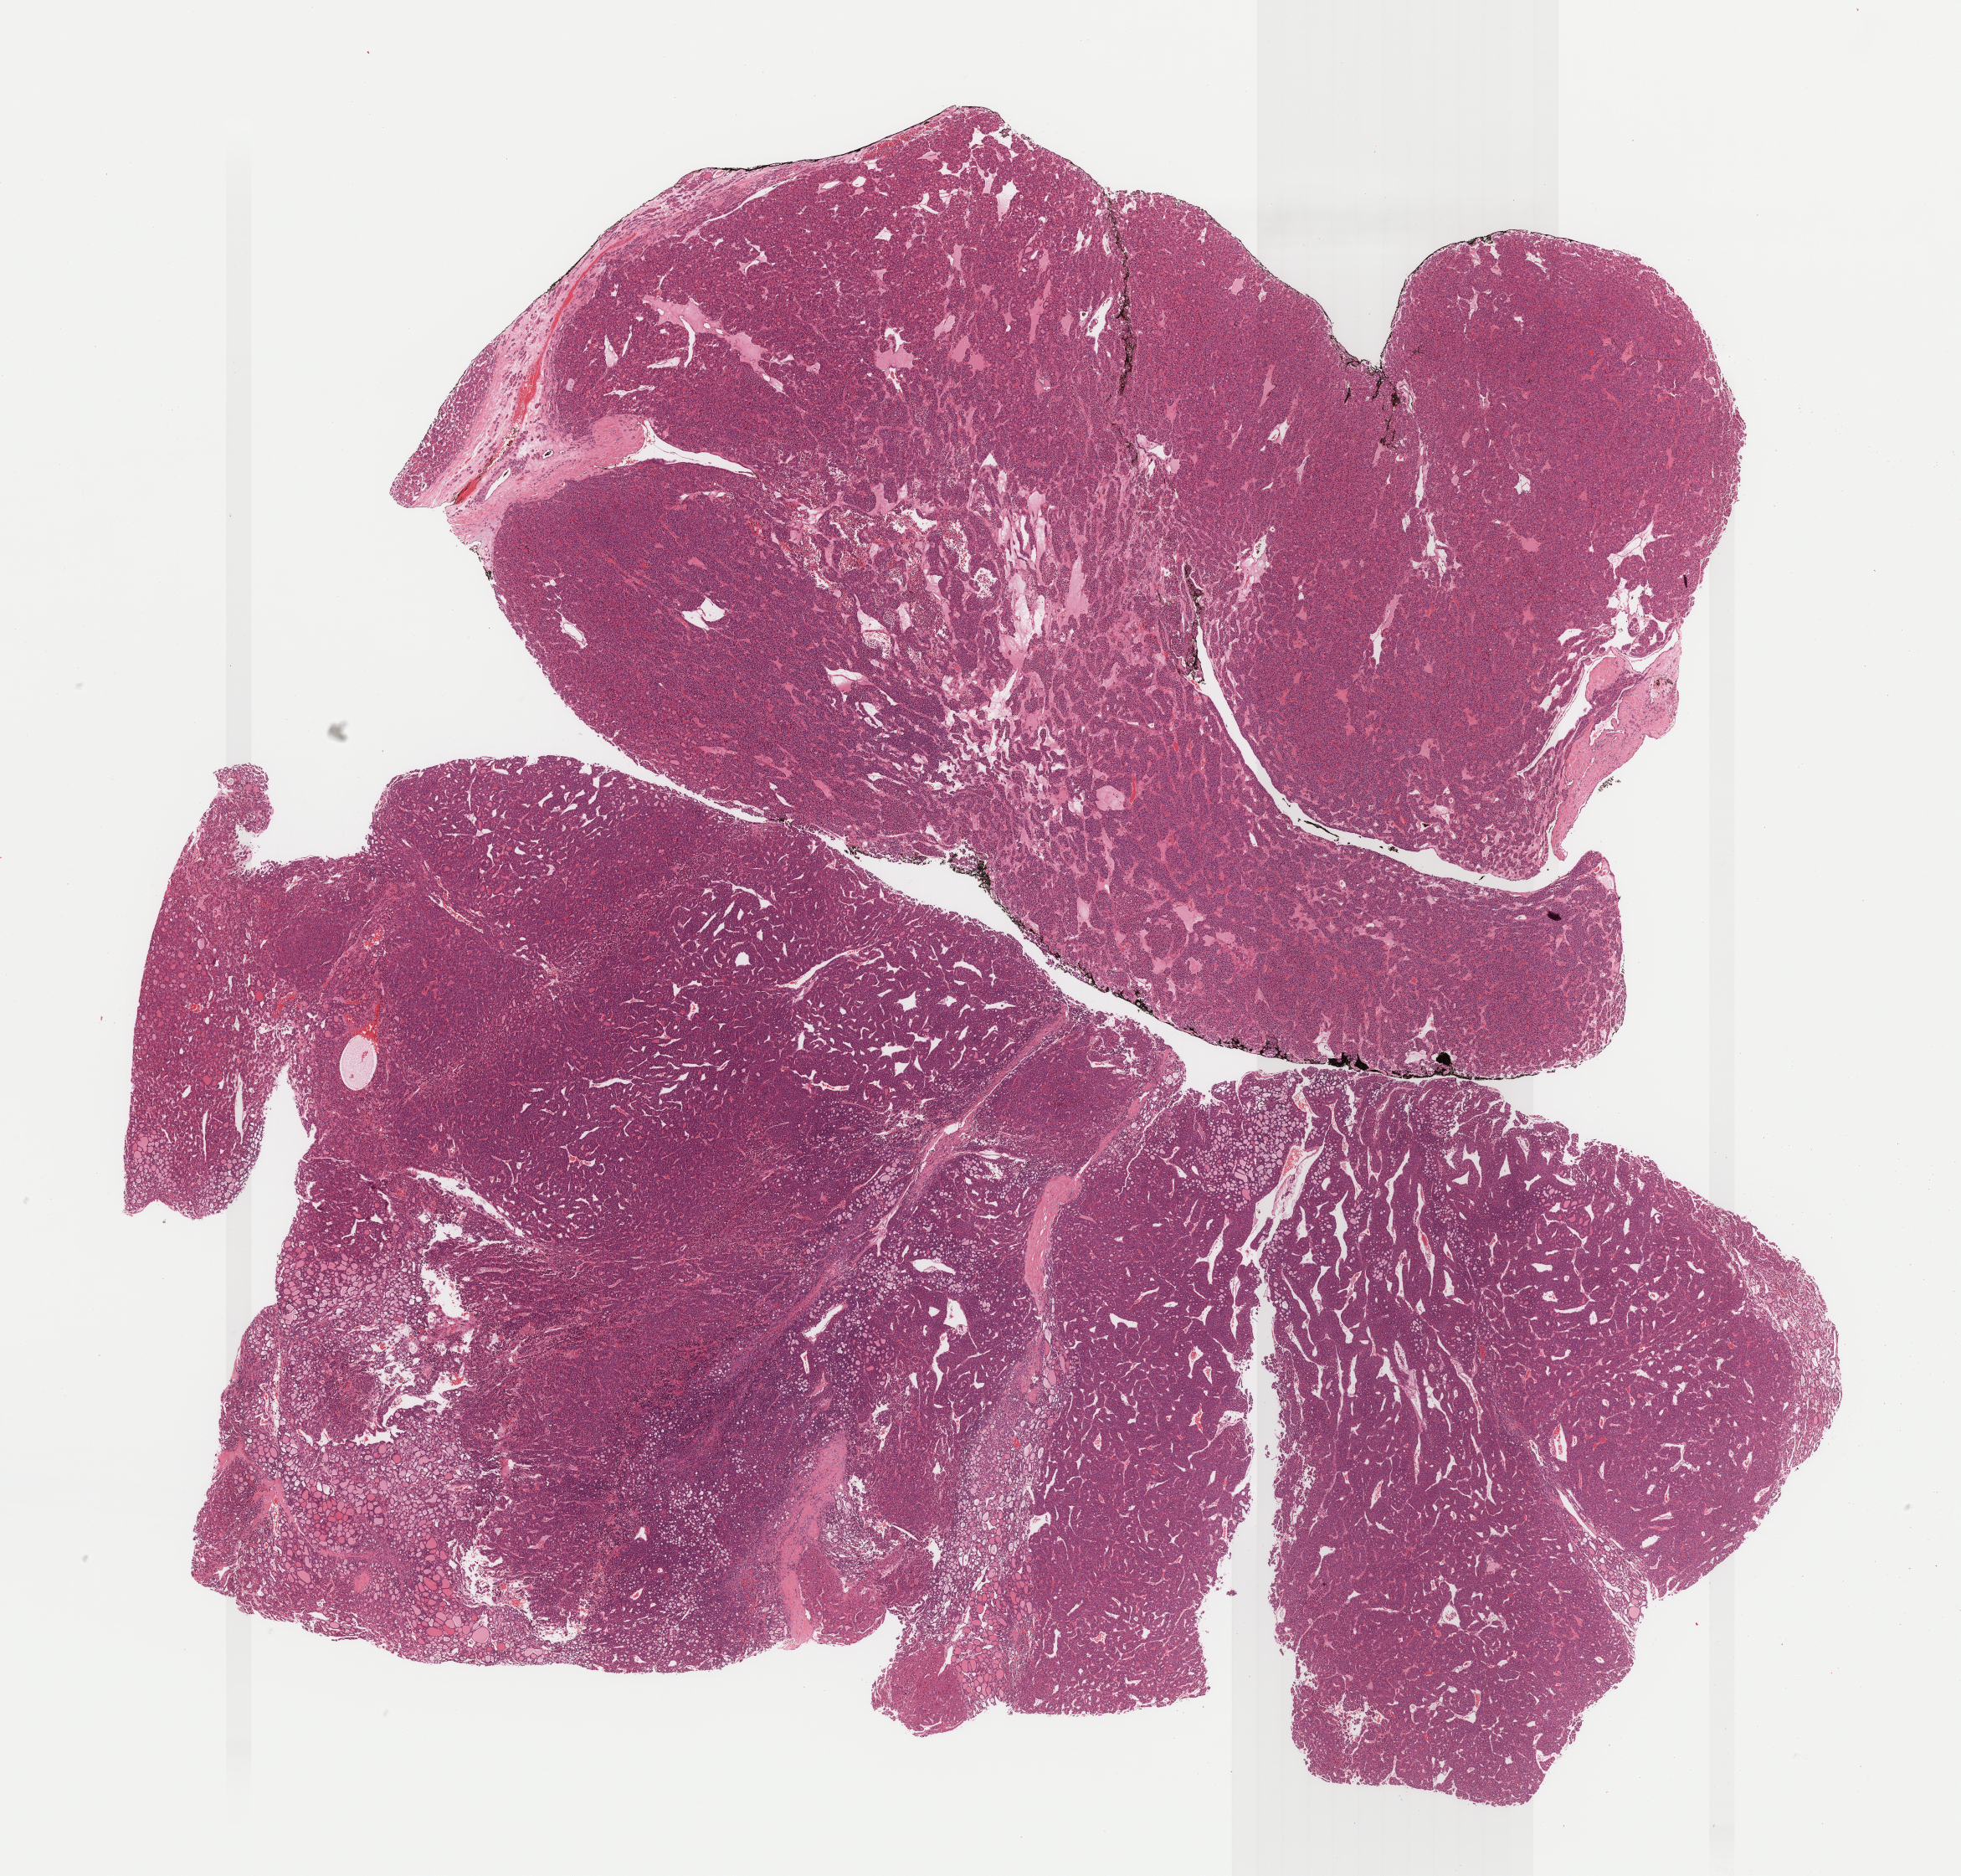
Digitized Hematoxylin and eosin (H&E) stained tissue section (whole slide), low-resolution overview of the scanned area, about 18.9 x 18.1 mm (slide scanned at 40x); FFPE section; thyroid, primary tumour sample. Female patient; age at initial diagnosis 62 years.
* laterality: left
* AJCC pathologic stage: III (7th edition)
* histologic diagnosis: Carcinoma, NOS
* lymph nodes positive (case pathology): 0 of 3 examined